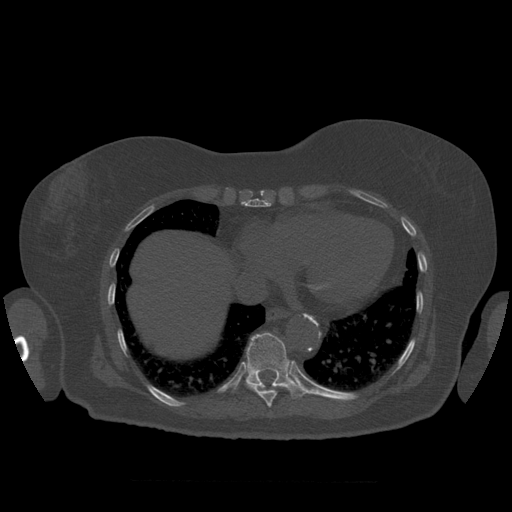
CT including the spine, one axial slice. 120 kVp. Bone window (W 1800 / L 400 HU). 1.25 mm slice thickness. 512 × 512 image matrix, field of view 404 × 404 mm. Patient age 81 years. From the clinical record (not read from this slice): primary cancer: renal.
Annotated regions visible in this slice (semi-automatically segmented with operator editing):
- T10 vertebra: bounding box [x1, y1, x2, y2] px = [245, 333, 308, 399]
- T9 vertebra: [246, 383, 277, 408]